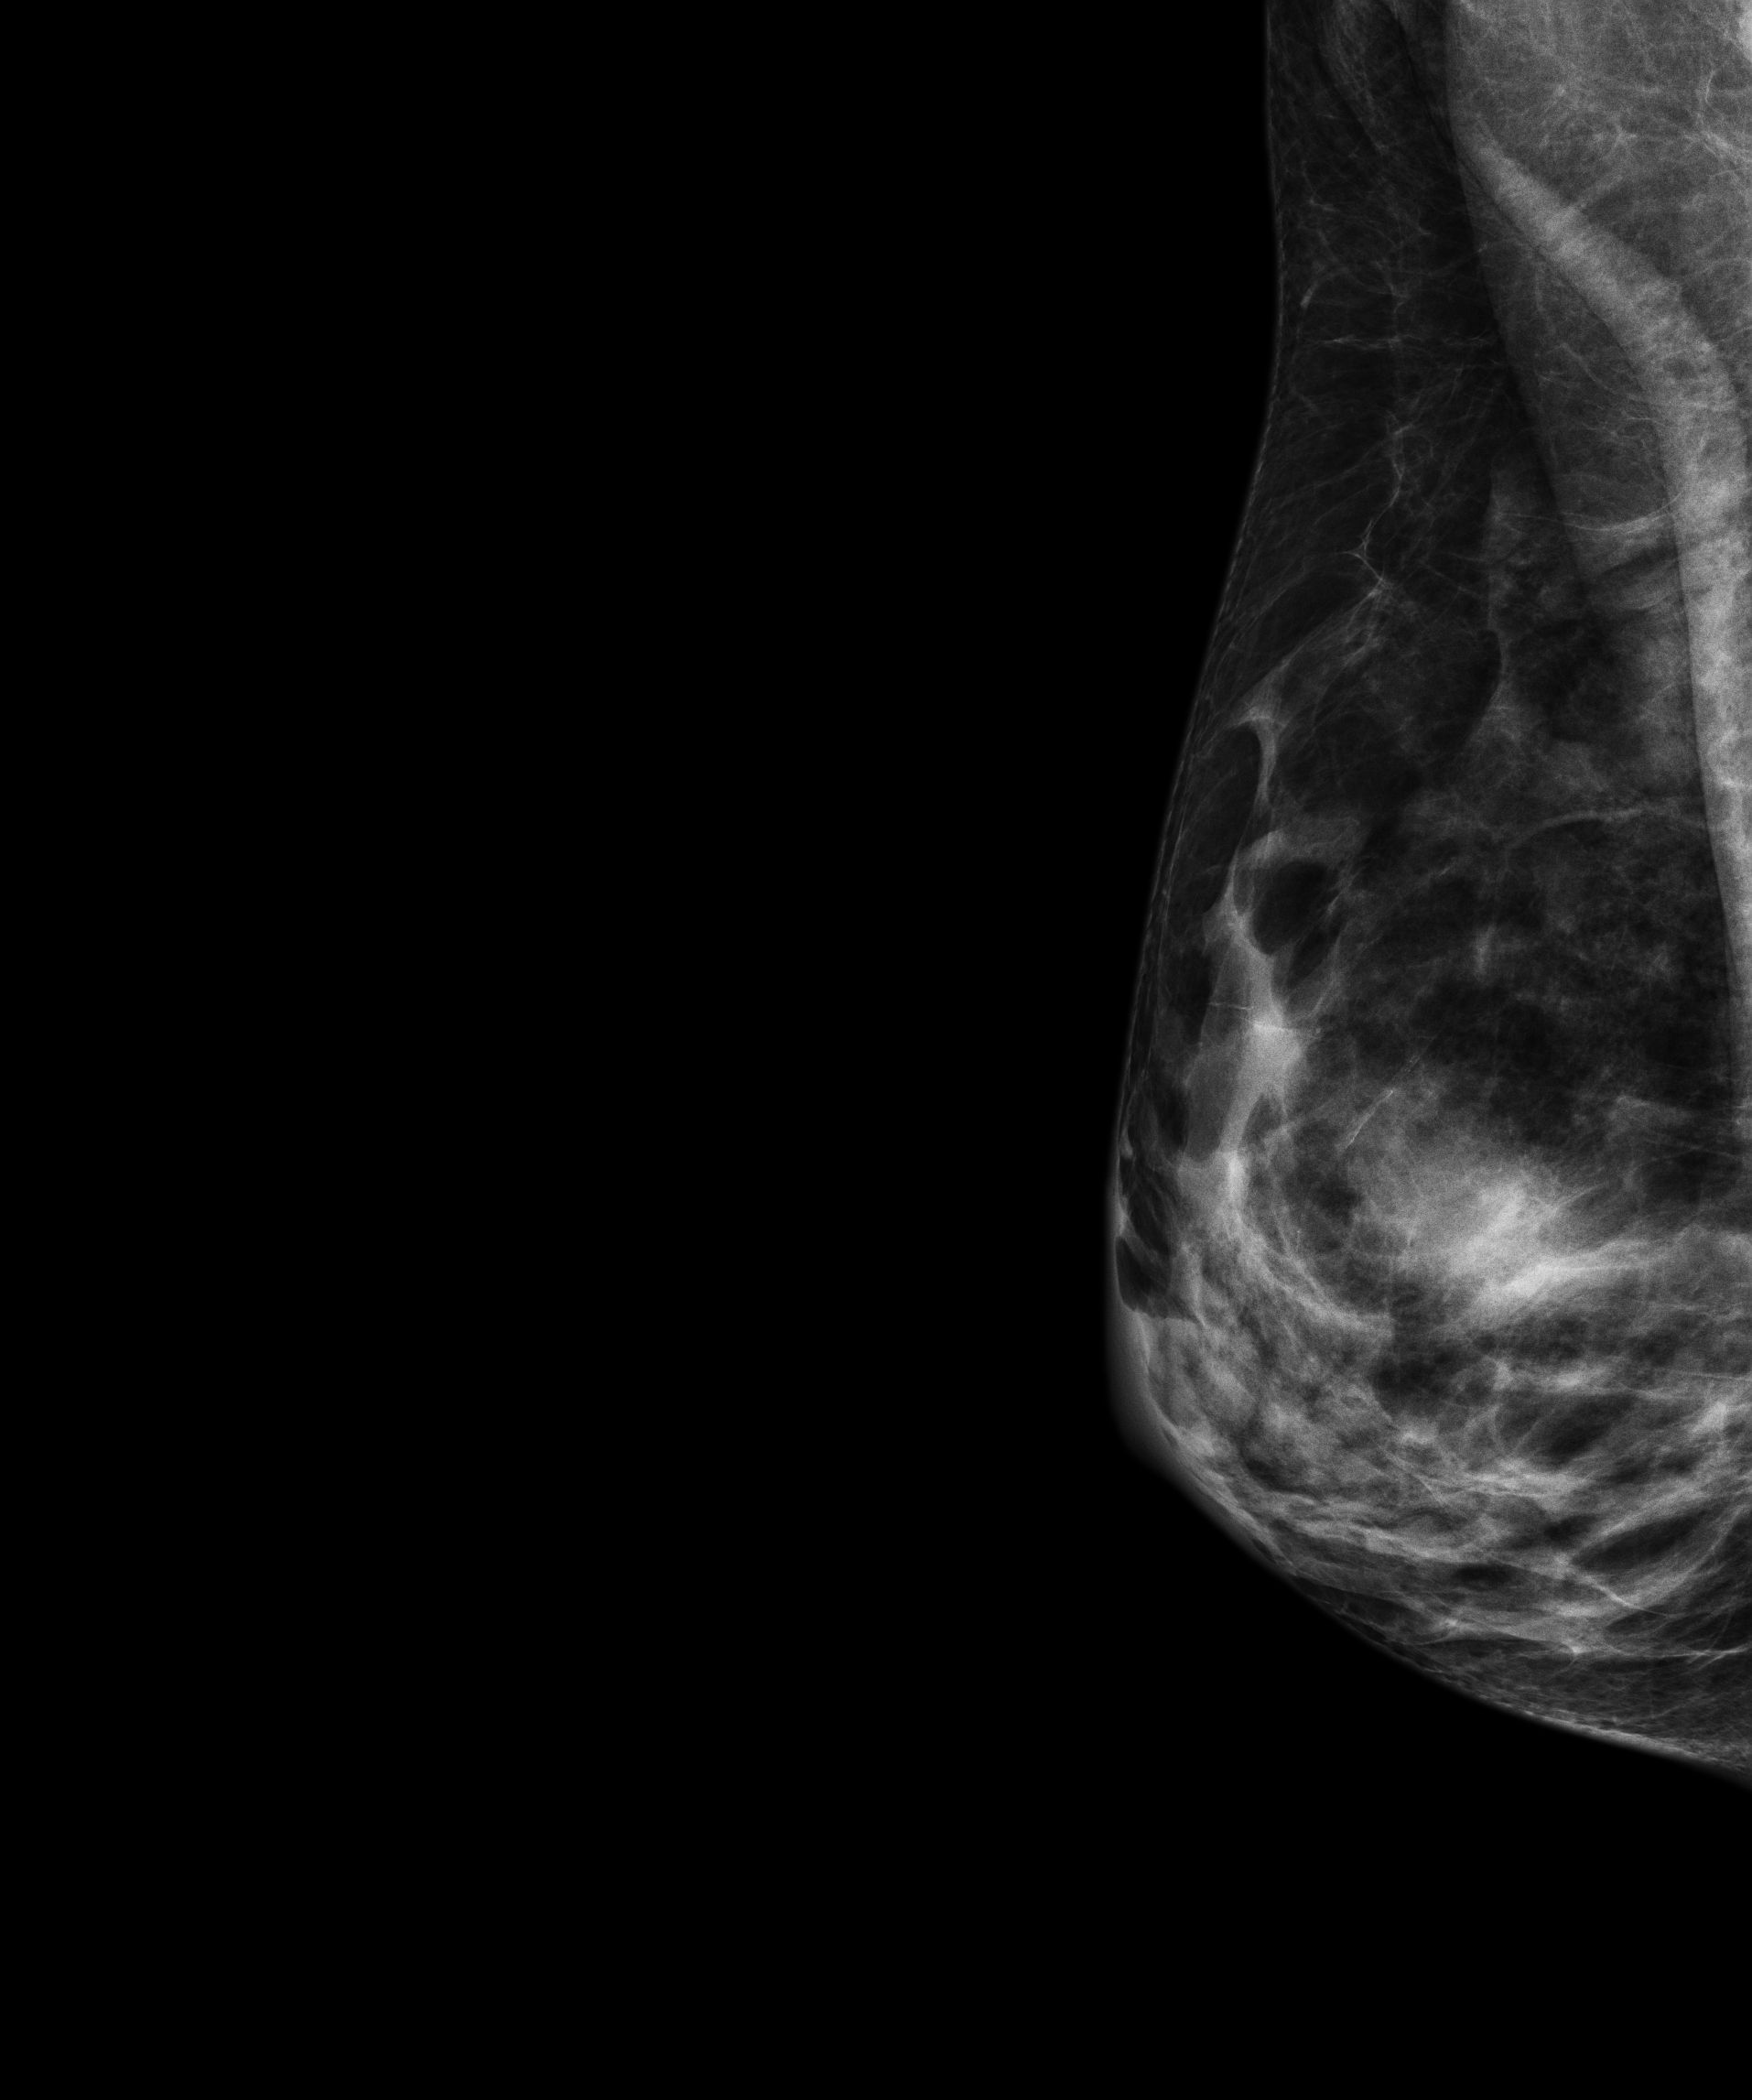
Annual screening mammography examination. Patient aged 67 years (female).
Image type: full-field digital mammogram. Breast: right. Projection: medio-lateral oblique projection.